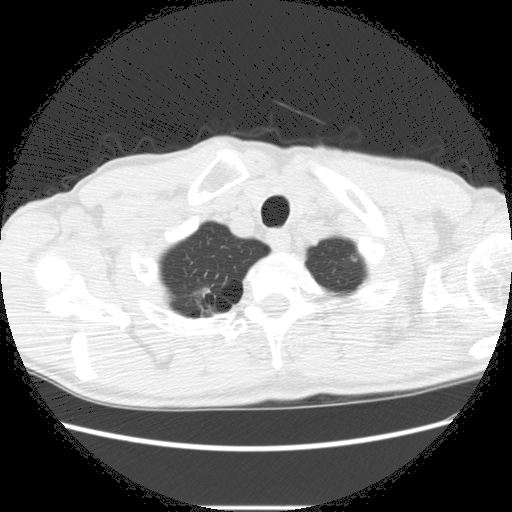
Axial slice from a low-dose chest CT screening exam. Second annual screen. Lung window (W 1500 / L -600 HU). Standard (soft-tissue) reconstruction kernel (STANDARD). Slice 19 of 282 in the series. 512 × 512 image matrix, field of view 360 × 360 mm. Male, age 66 years at enrolment. Former smoker at enrolment.
Expert-annotated lung lesion, bounding box (x1, y1, x2, y2) in pixels: (169, 274, 237, 329). The screening reader recorded 5 non-calcified nodules or masses ≥4 mm on this exam (right lower lobe, right upper lobe, right upper lobe, right upper lobe, left lower lobe); which of them this box marks is not recorded. Official screen result: positive, change unspecified: nodule(s) >= 4 mm or enlarging nodule(s), mass(es), or other non-specific abnormalities suspicious for lung cancer. Lung cancer was diagnosed 75 days after this screen: adenocarcinoma, NOS, right upper lobe, undifferentiated (G4), stage IA (AJCC 6th edition), 20 mm at pathology.